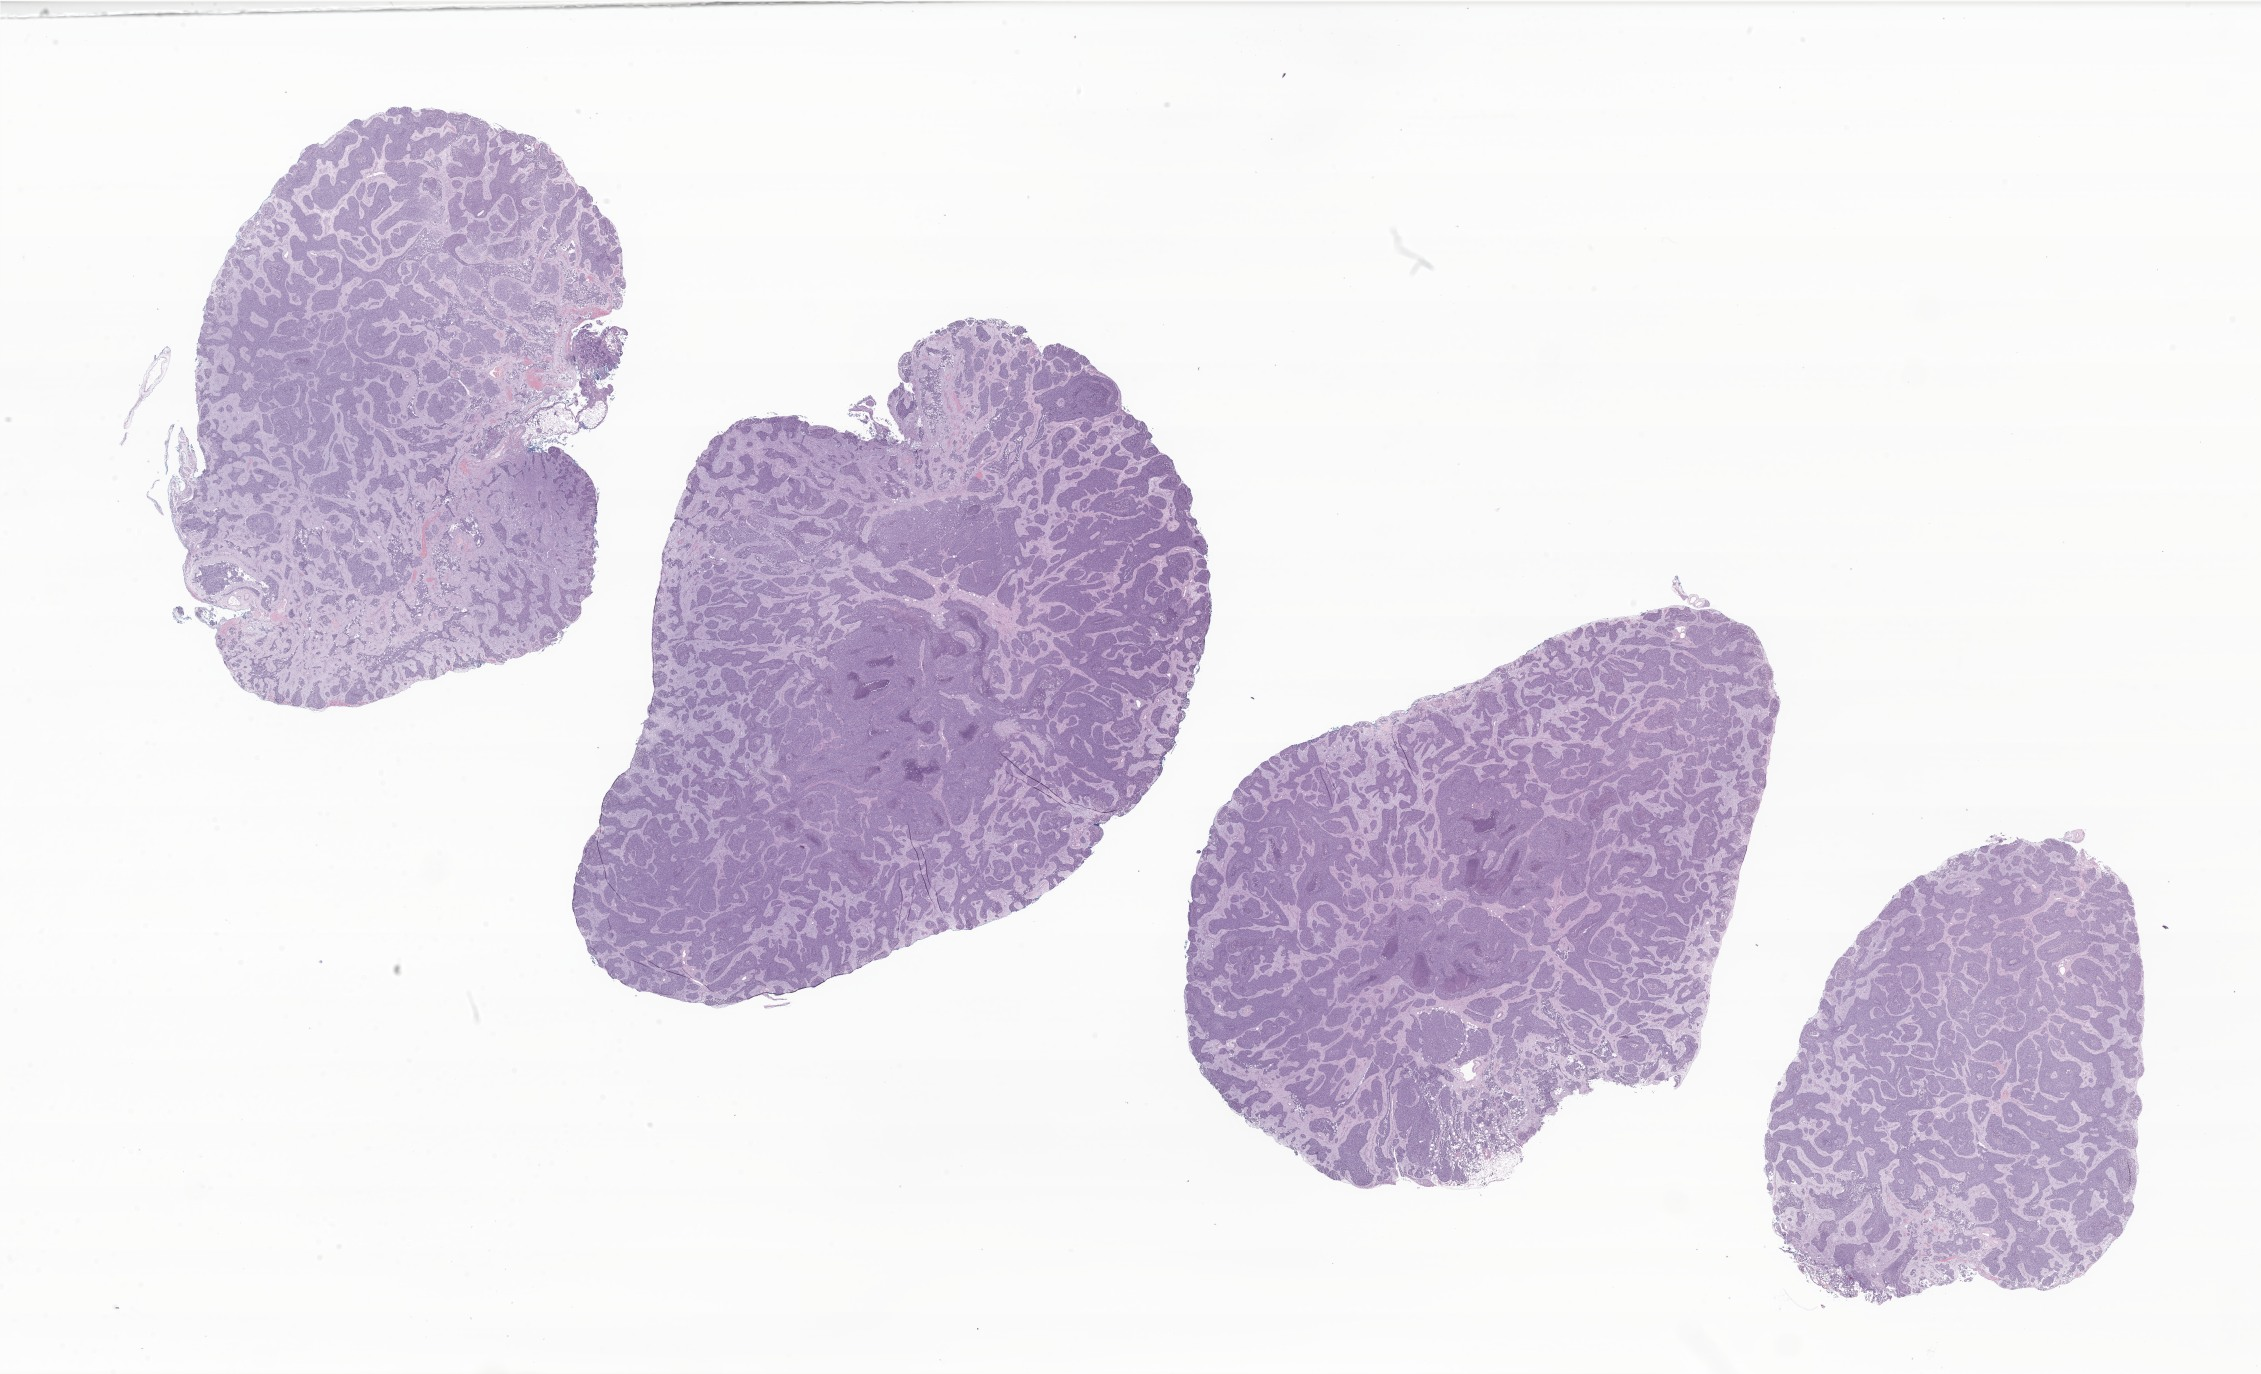
Whole-slide image, hematoxylin and eosin (H&E) stain of tumor tissue from the abdomen, whole scanned area (about 38.1 x 23.2 mm) shown as a low-resolution overview. FFPE section. Patient male; age 254 months.
Recorded diagnosis: Desmoplastic small round cell tumor.